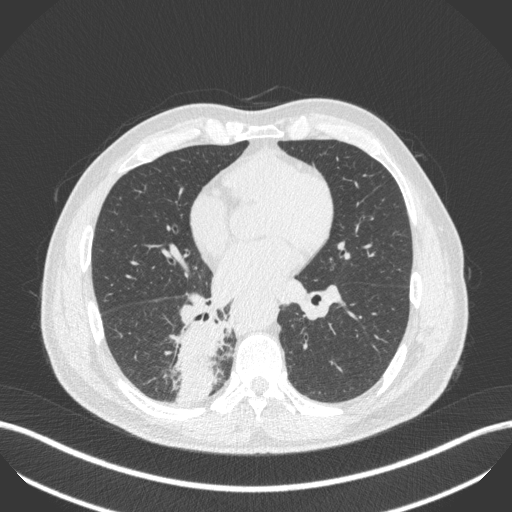
Chest CT, one axial slice. Position 221 of 451 along the scan axis. Reconstruction kernel B31f. Lung window (W 1500 / L -600 HU). 1 mm slice thickness. 512 × 512 image matrix, field of view 400 × 400 mm. Patient: male, 61 years. Case-level facts recorded for this patient, not image findings: clinical TNM (as recorded): T1 N0 M0; histopathological grade: G3.
Annotated regions visible in this slice (bounding box drawn by a radiologist):
- lung tumour (recorded histology: small cell carcinoma): bounding box <169,310,222,405> (left, top, right, bottom; pixels)